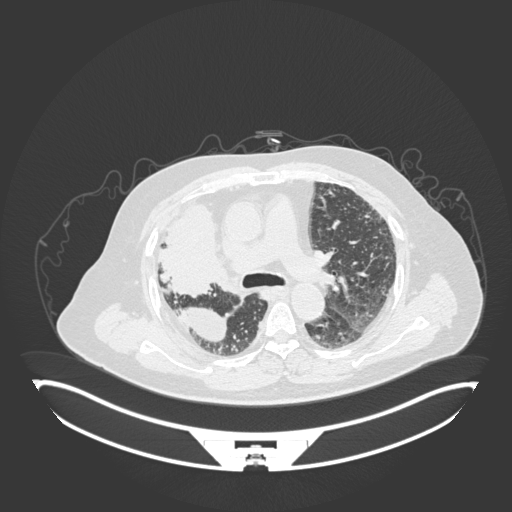
Chest CT, one axial slice; slice 111 of 201 in the series (ordered by position); 120 kVp; lung window (W 1500 / L -600 HU); 1 mm slice thickness; 512 × 512 image matrix. Patient: male, 69 years. From the clinical record (not read from this slice): clinical TNM (as recorded): T4 N3 M1.
Outlined on this slice (bounding box drawn by a radiologist):
- lung tumour (recorded histology: adenocarcinoma): bounding box [x1, y1, x2, y2] px = [156, 200, 230, 306]